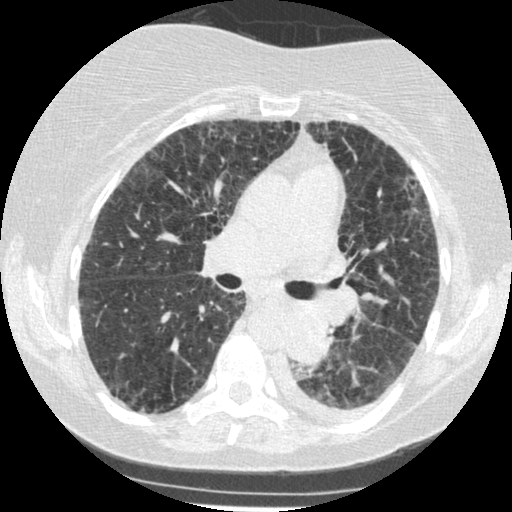
Low-dose screening chest CT, one axial slice. Slice 151 of 341 in the series (ordered by position). Reconstruction kernel STANDARD. Lung window (W 1500 / L -600 HU). 1.25 mm slice thickness. 512 × 512 image matrix, field of view 310 × 310 mm.
Structures marked on this image (manually delineated by an expert):
- lesion 1 (tumor, lower lobe of left lung): bounding box [x1, y1, x2, y2] px = [287, 309, 332, 366]